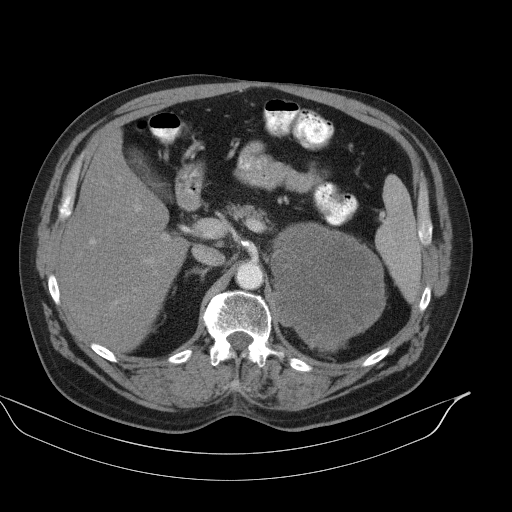
Contrast-enhanced abdominal CT, one axial slice; slice 67 of 92 in the series (ordered by position); 130 kVp; intravenous contrast given; soft-tissue window (W 400 / L 40 HU); 5 mm slice thickness; 512 × 512 image matrix, field of view 449 × 449 mm. Patient: male, 56 years. Case-level facts recorded for this patient, not image findings: diagnosis: adrenocortical carcinoma; tumour side: left adrenal; tumour size at pathology: 15 cm; Ki-67 index: 35 %; stage (as recorded): 4.
Annotated regions visible in this slice (semi-automatic segmentation, software-assisted and operator-edited):
- mass: box from (x=272, y=224) to (x=383, y=349) px